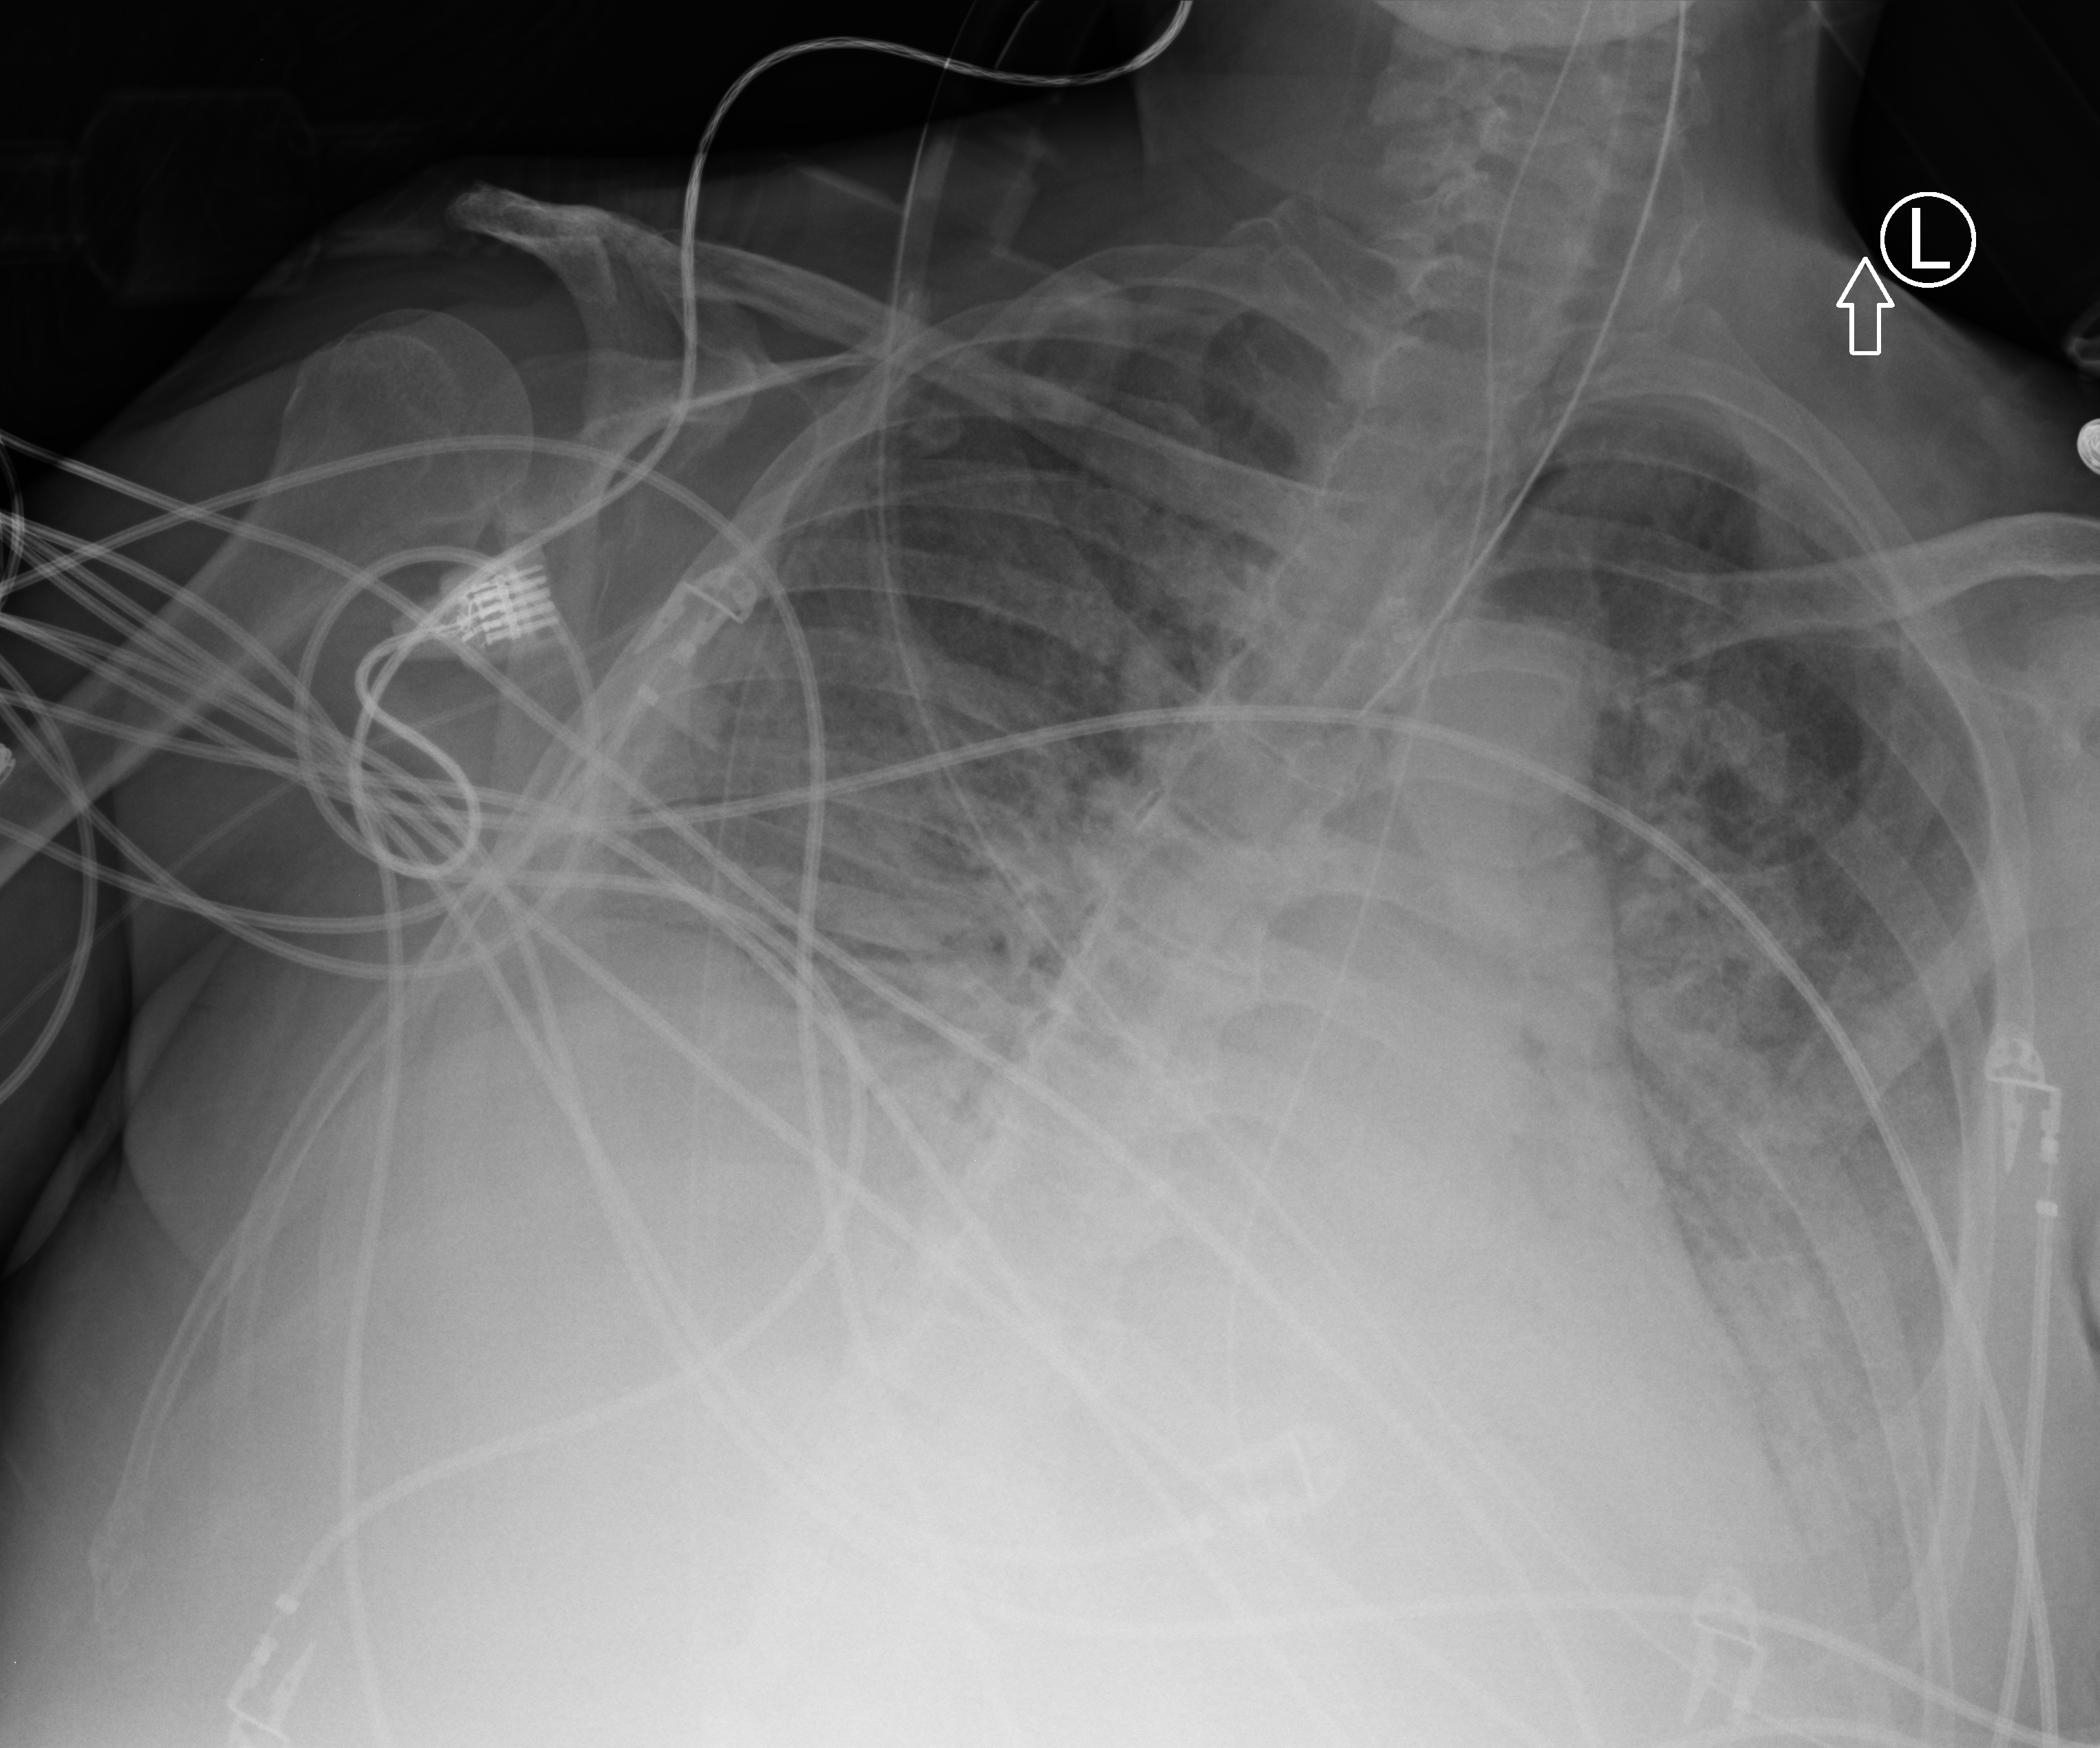
Portable chest radiograph, anteroposterior (AP) projection. Male patient hospitalised with COVID-19, age 60–74 years.
From the hospital-stay record, not from the radiograph (when in the stay this image was taken is not recorded): COPD (admission record): no; chronic kidney disease (admission record): no.